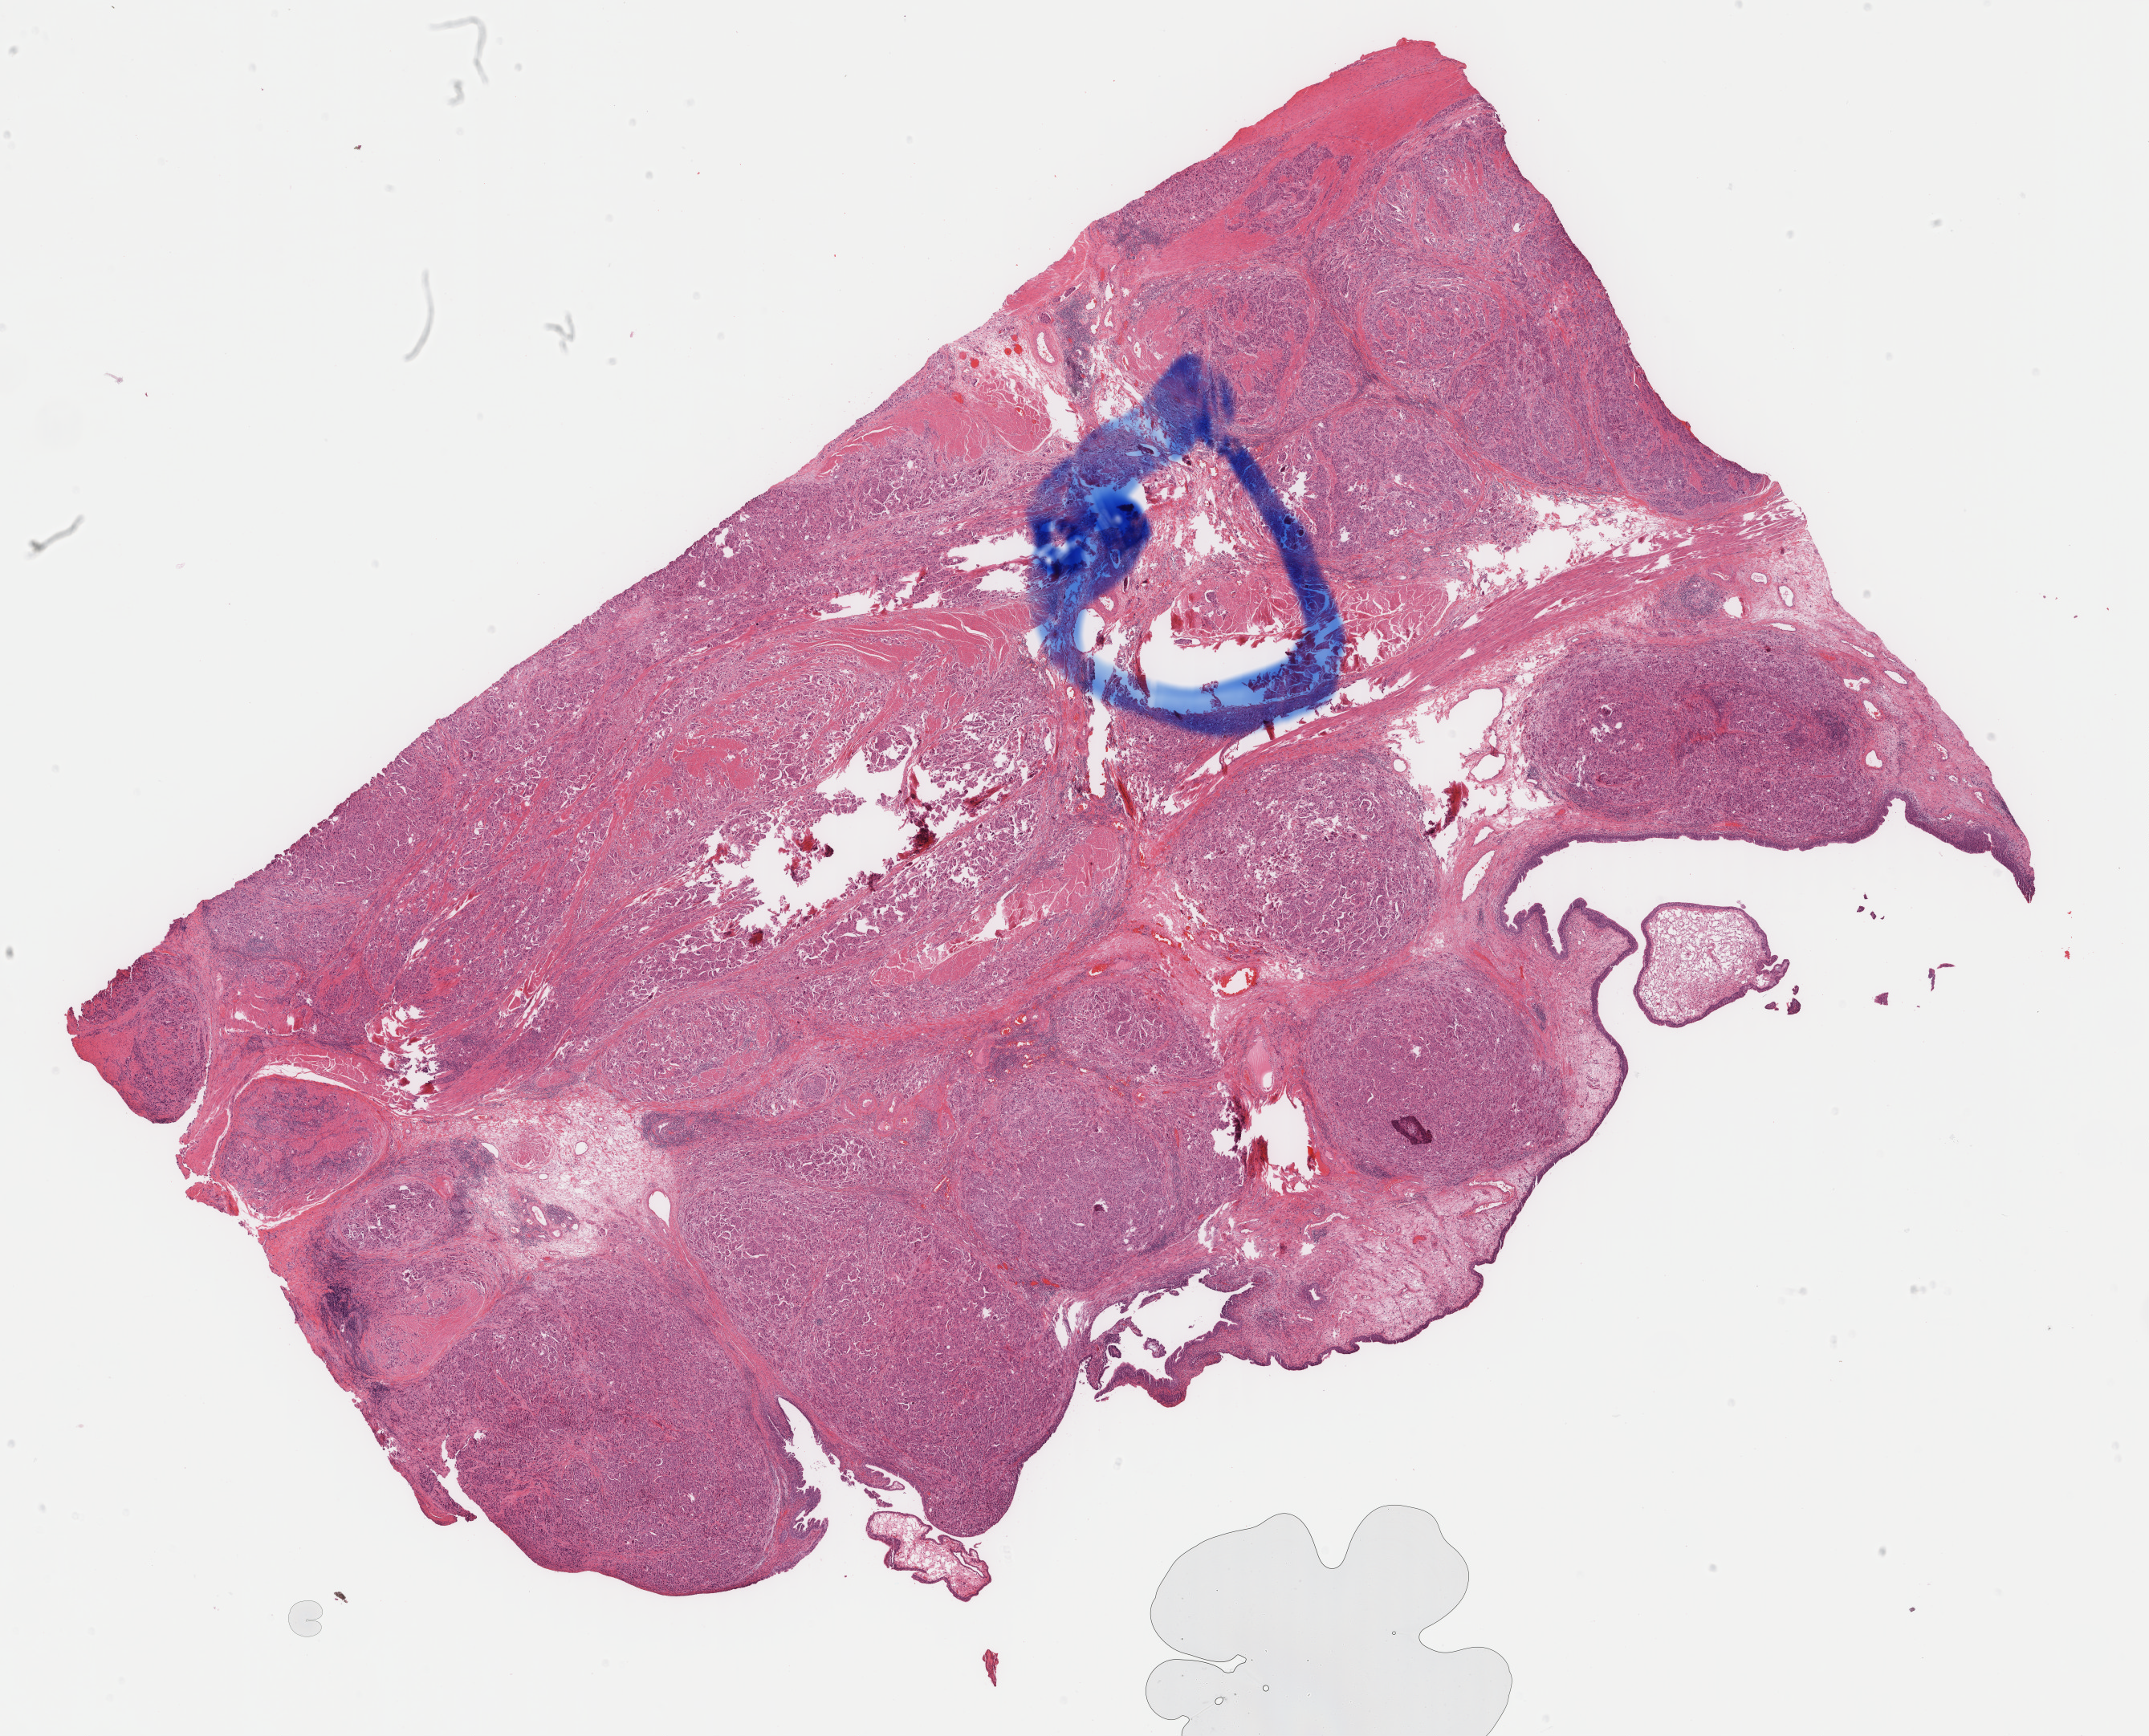
Whole-slide histology image, Hematoxylin and eosin (H&E) stained — a low-resolution overview of the entire scanned area, about 21.2 x 17.2 mm (slide scanned at 40x), formalin-fixed paraffin-embedded (FFPE) diagnostic section, sample: primary tumour, bladder. Male, age 76 years at initial diagnosis. Histologic grade: high grade.
* lymph nodes positive (case pathology): 8 of 17 examined
* AJCC pathologic stage: IV (7th edition)
* histologic diagnosis: Transitional cell carcinoma
* TNM: T3b N2 MX